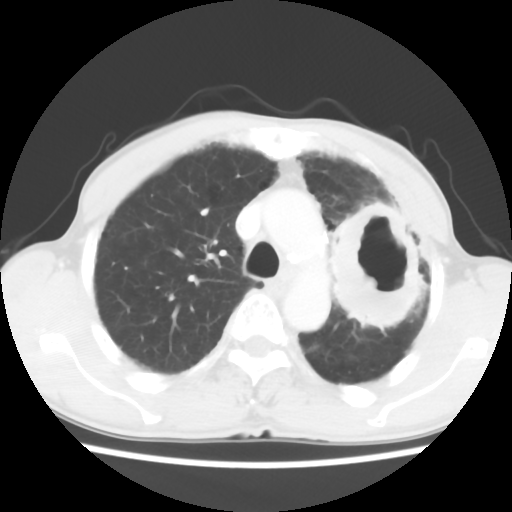
Chest CT, one axial slice. Slice 43 of 60 in the series (ordered by position). 120 kVp. Lung window (W 1500 / L -600 HU). 512 × 512 image matrix, field of view 308 × 308 mm. Patient: male, 64 years. From the clinical record (not read from this slice): clinical TNM (as recorded): T3 N3 M0; histopathological grade: G3.
Outlined on this slice (rectangle marked by the reading radiologist):
- lung tumour (recorded histology: adenocarcinoma): bounding box (x1, y1, x2, y2) in pixels: (323, 191, 436, 346)